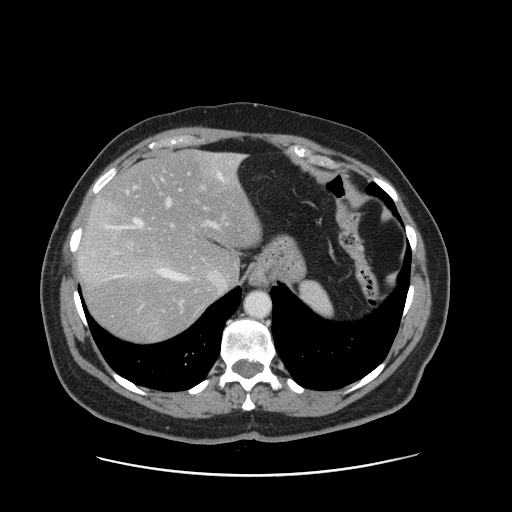
Contrast-enhanced abdominal CT, one axial slice. Slice 117 of 161 in the series (ordered by position). 120 kVp. Intravenous contrast given. Soft-tissue window (W 400 / L 40 HU). 2.5 mm slice thickness. 512 × 512 image matrix. Female patient, age 62 years. Case-level facts recorded for this patient, not image findings: diagnosis: colorectal cancer liver metastases, imaged before liver resection; multiple liver metastases: no; largest metastasis: 2.5 cm; disease in both lobes: no.
Annotated regions visible in this slice (outlined manually by an expert reader):
- hepatic veins: bounding box <105,156,241,282> (left, top, right, bottom; pixels)
- liver: <77,151,262,344>
- planned liver remnant (the part of the liver to remain after resection): <95,151,261,283>
- portal vein (with intrahepatic branches): <163,171,220,304>